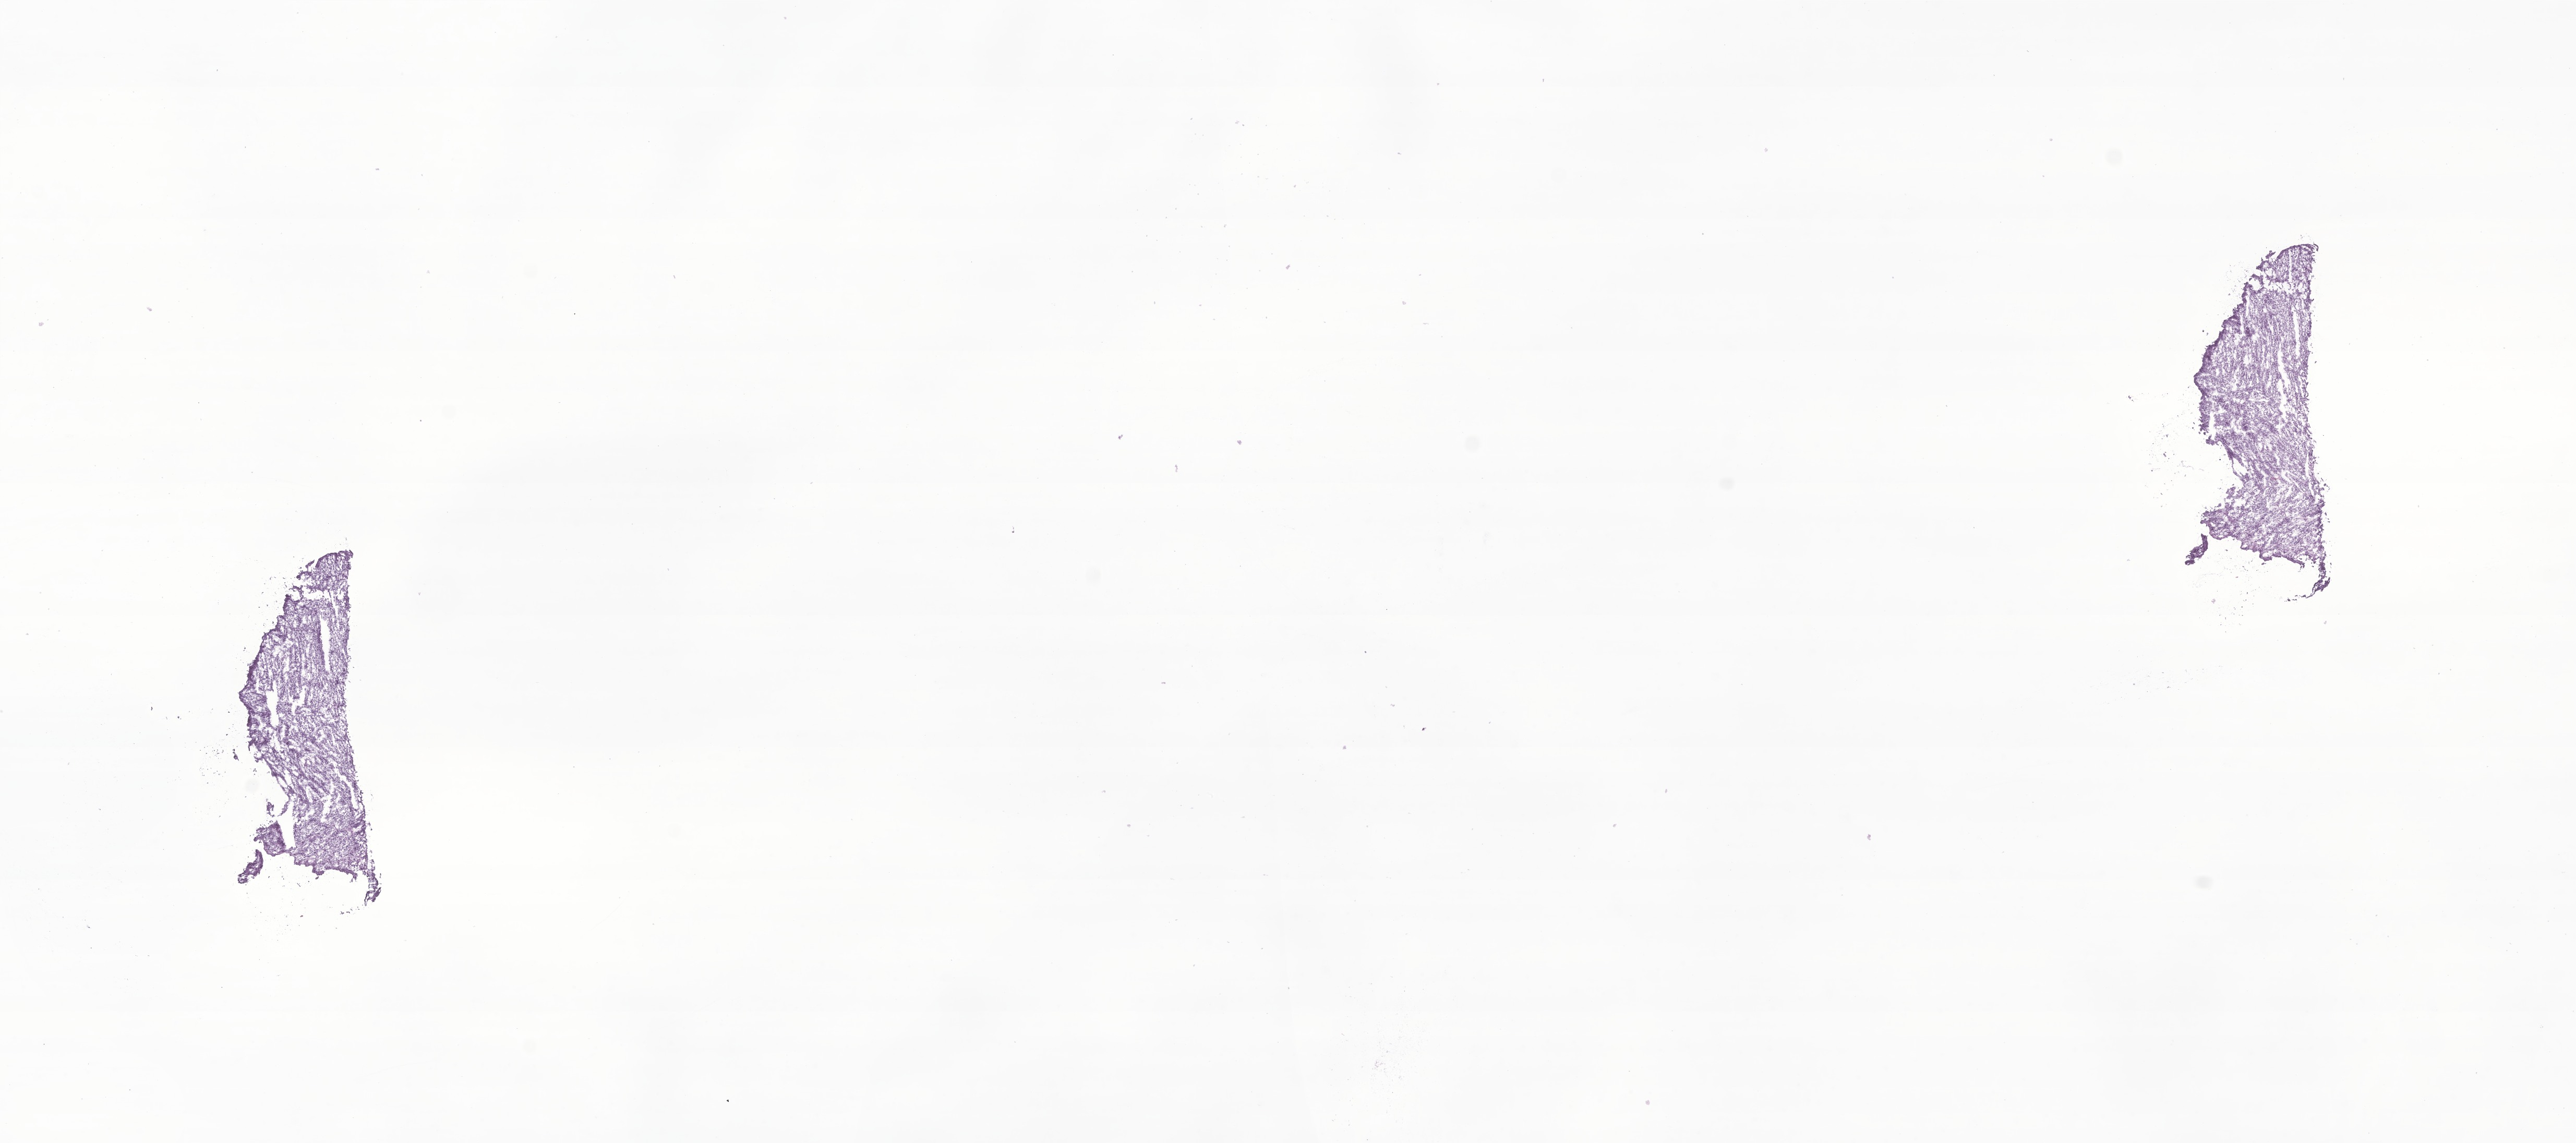
Digitized H&E-stained section of tumor tissue from the eye, shown as a low-resolution overview of the whole scanned area (about 20.8 x 9.2 mm). Frozen section. Patient male; age 68 months (5 years 8 months).
Diagnosis (ICD-O-3 morphology term): Embryonal rhabdomyosarcoma, NOS.